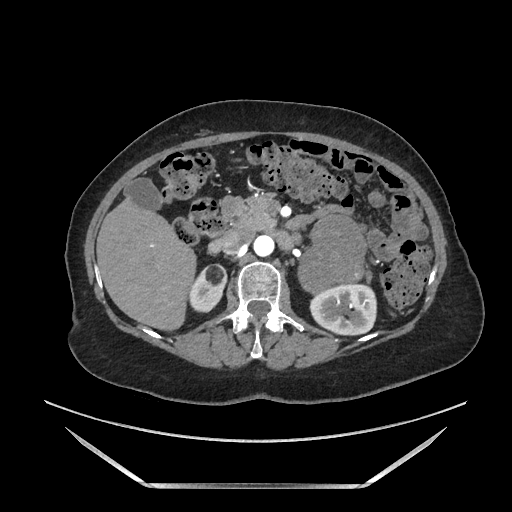
Contrast-enhanced abdominal CT, one axial slice; slice 92 of 205 in the series (ordered by position); soft-tissue window (W 400 / L 40 HU); 512 × 512 image matrix, field of view 440 × 440 mm. Female patient. From the clinical record (not read from this slice): diagnosis: adrenocortical carcinoma; tumour side: left adrenal; tumour size at pathology: 12.5 cm; Ki-67 index: 39 %; stage (as recorded): 3.
Outlined on this slice (semi-automatically segmented with operator editing):
- mass: bounding box <302,218,363,288> (left, top, right, bottom; pixels)